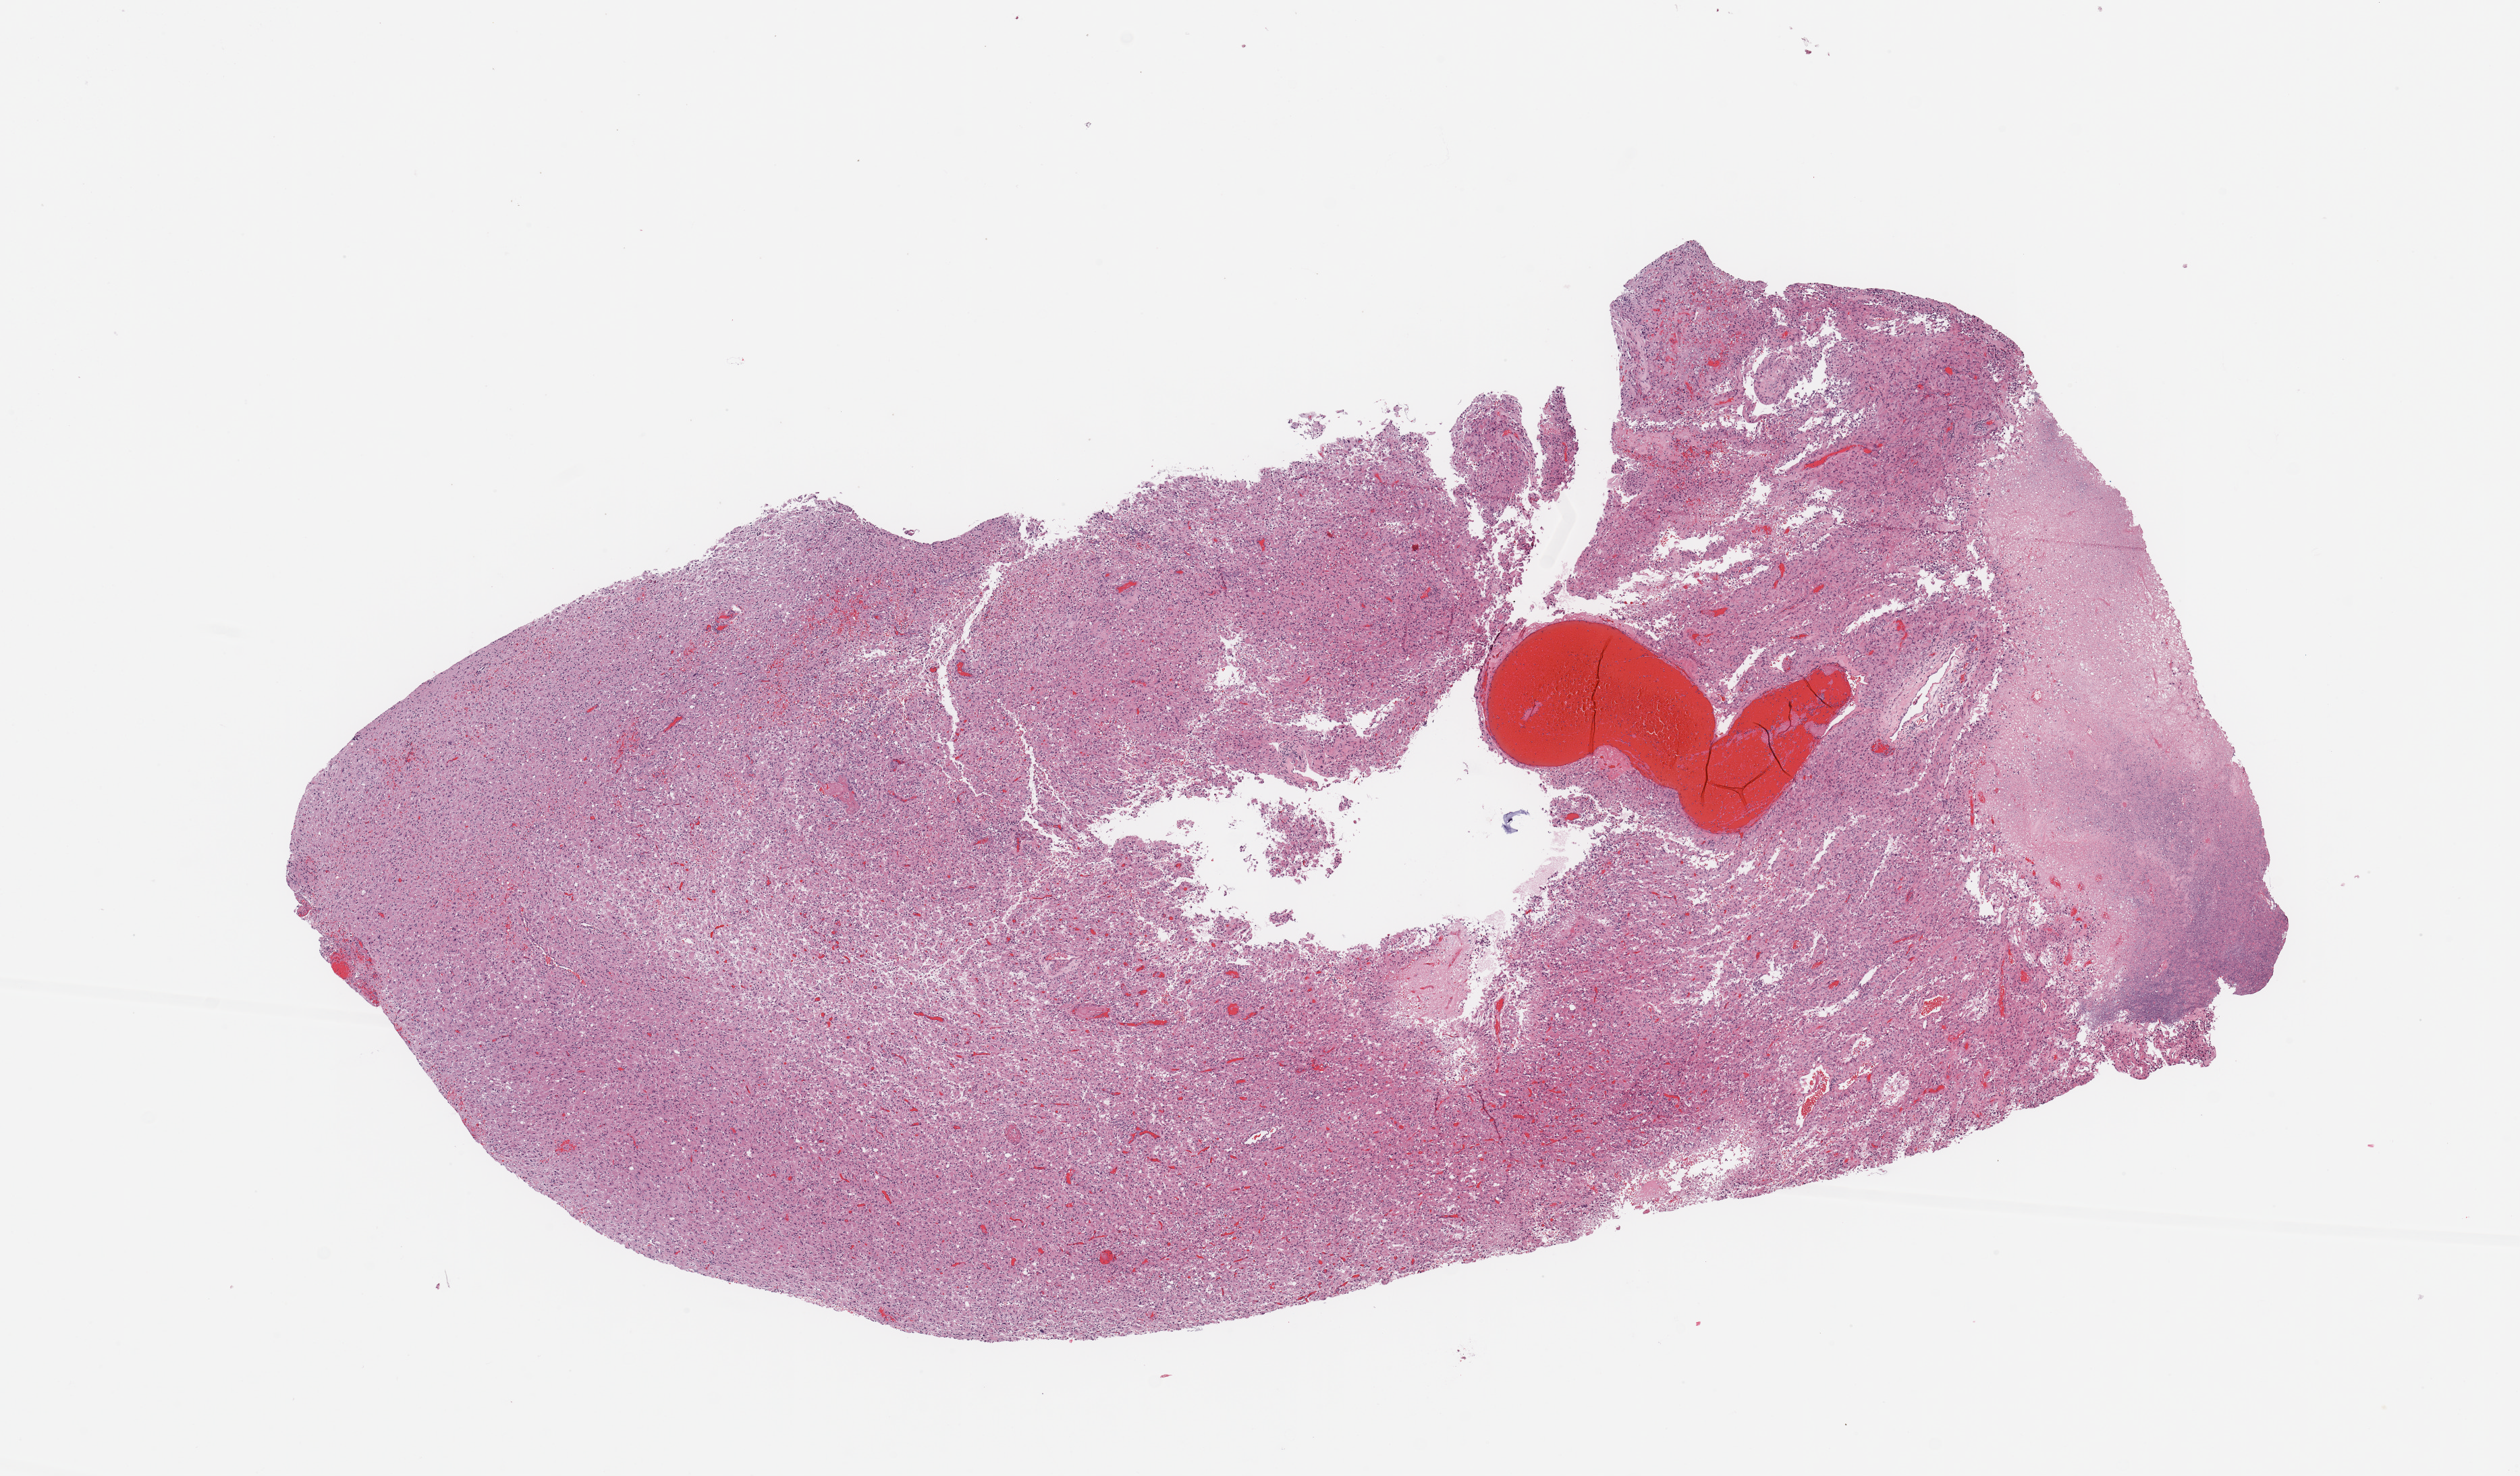
Digitized H&E tissue section (whole slide) — low-resolution overview of the scanned area, about 14.8 x 8.6 mm (from a 20x scan). Tumour tissue sample, brain. 62-year-old female patient.
Primary tumour site (as recorded): temporal lobe. Diagnosis: Glioblastoma.